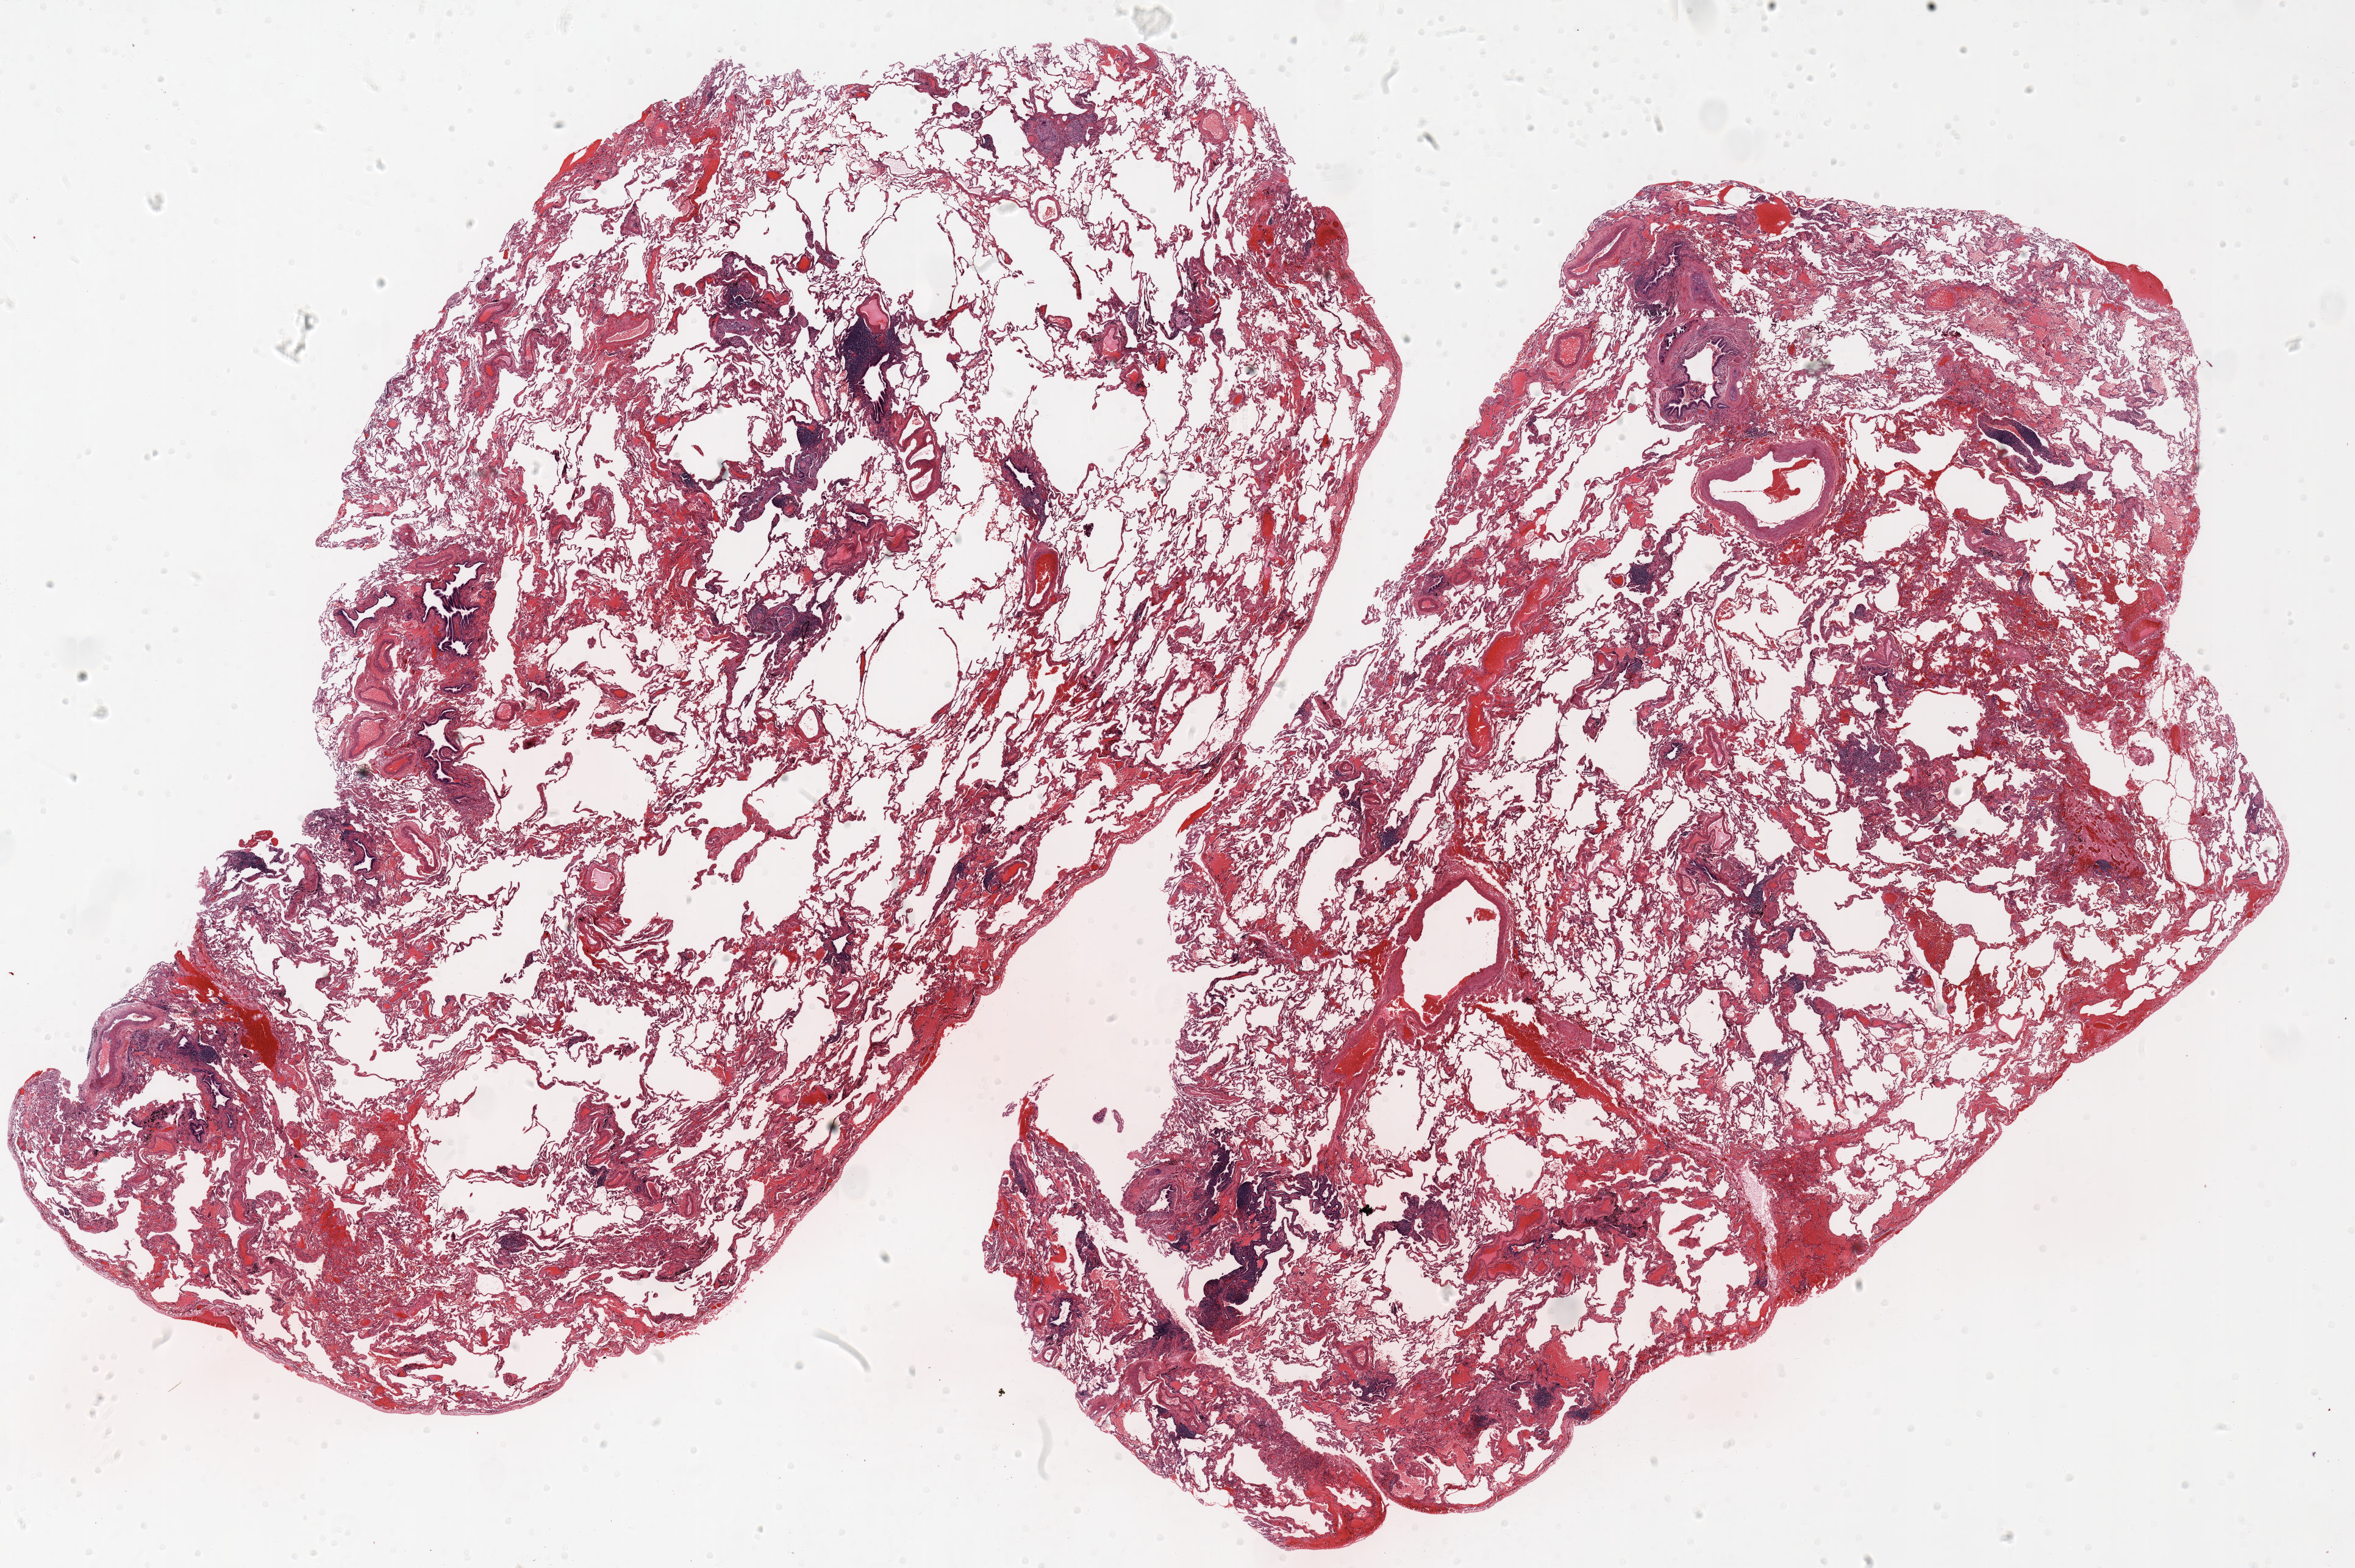
H&E-stained whole-slide image, shown as a low-resolution overview of the whole scanned area (about 31.0 x 20.7 mm), FFPE section, lung tissue. Female, age 72 at enrolment. Former smoker at enrolment. Grade: moderately differentiated (G2).
Participant's lung-cancer diagnosis: Adenocarcinoma, NOS. Primary tumour location (clinical record): left upper lobe. Stage (AJCC 6th edition): IA. Tumour size (pathology): 25 mm. ICD-O-3 topography: upper lobe of lung (C34.1). Note: participant had 2 primary lung cancers recorded; fields above describe the first.